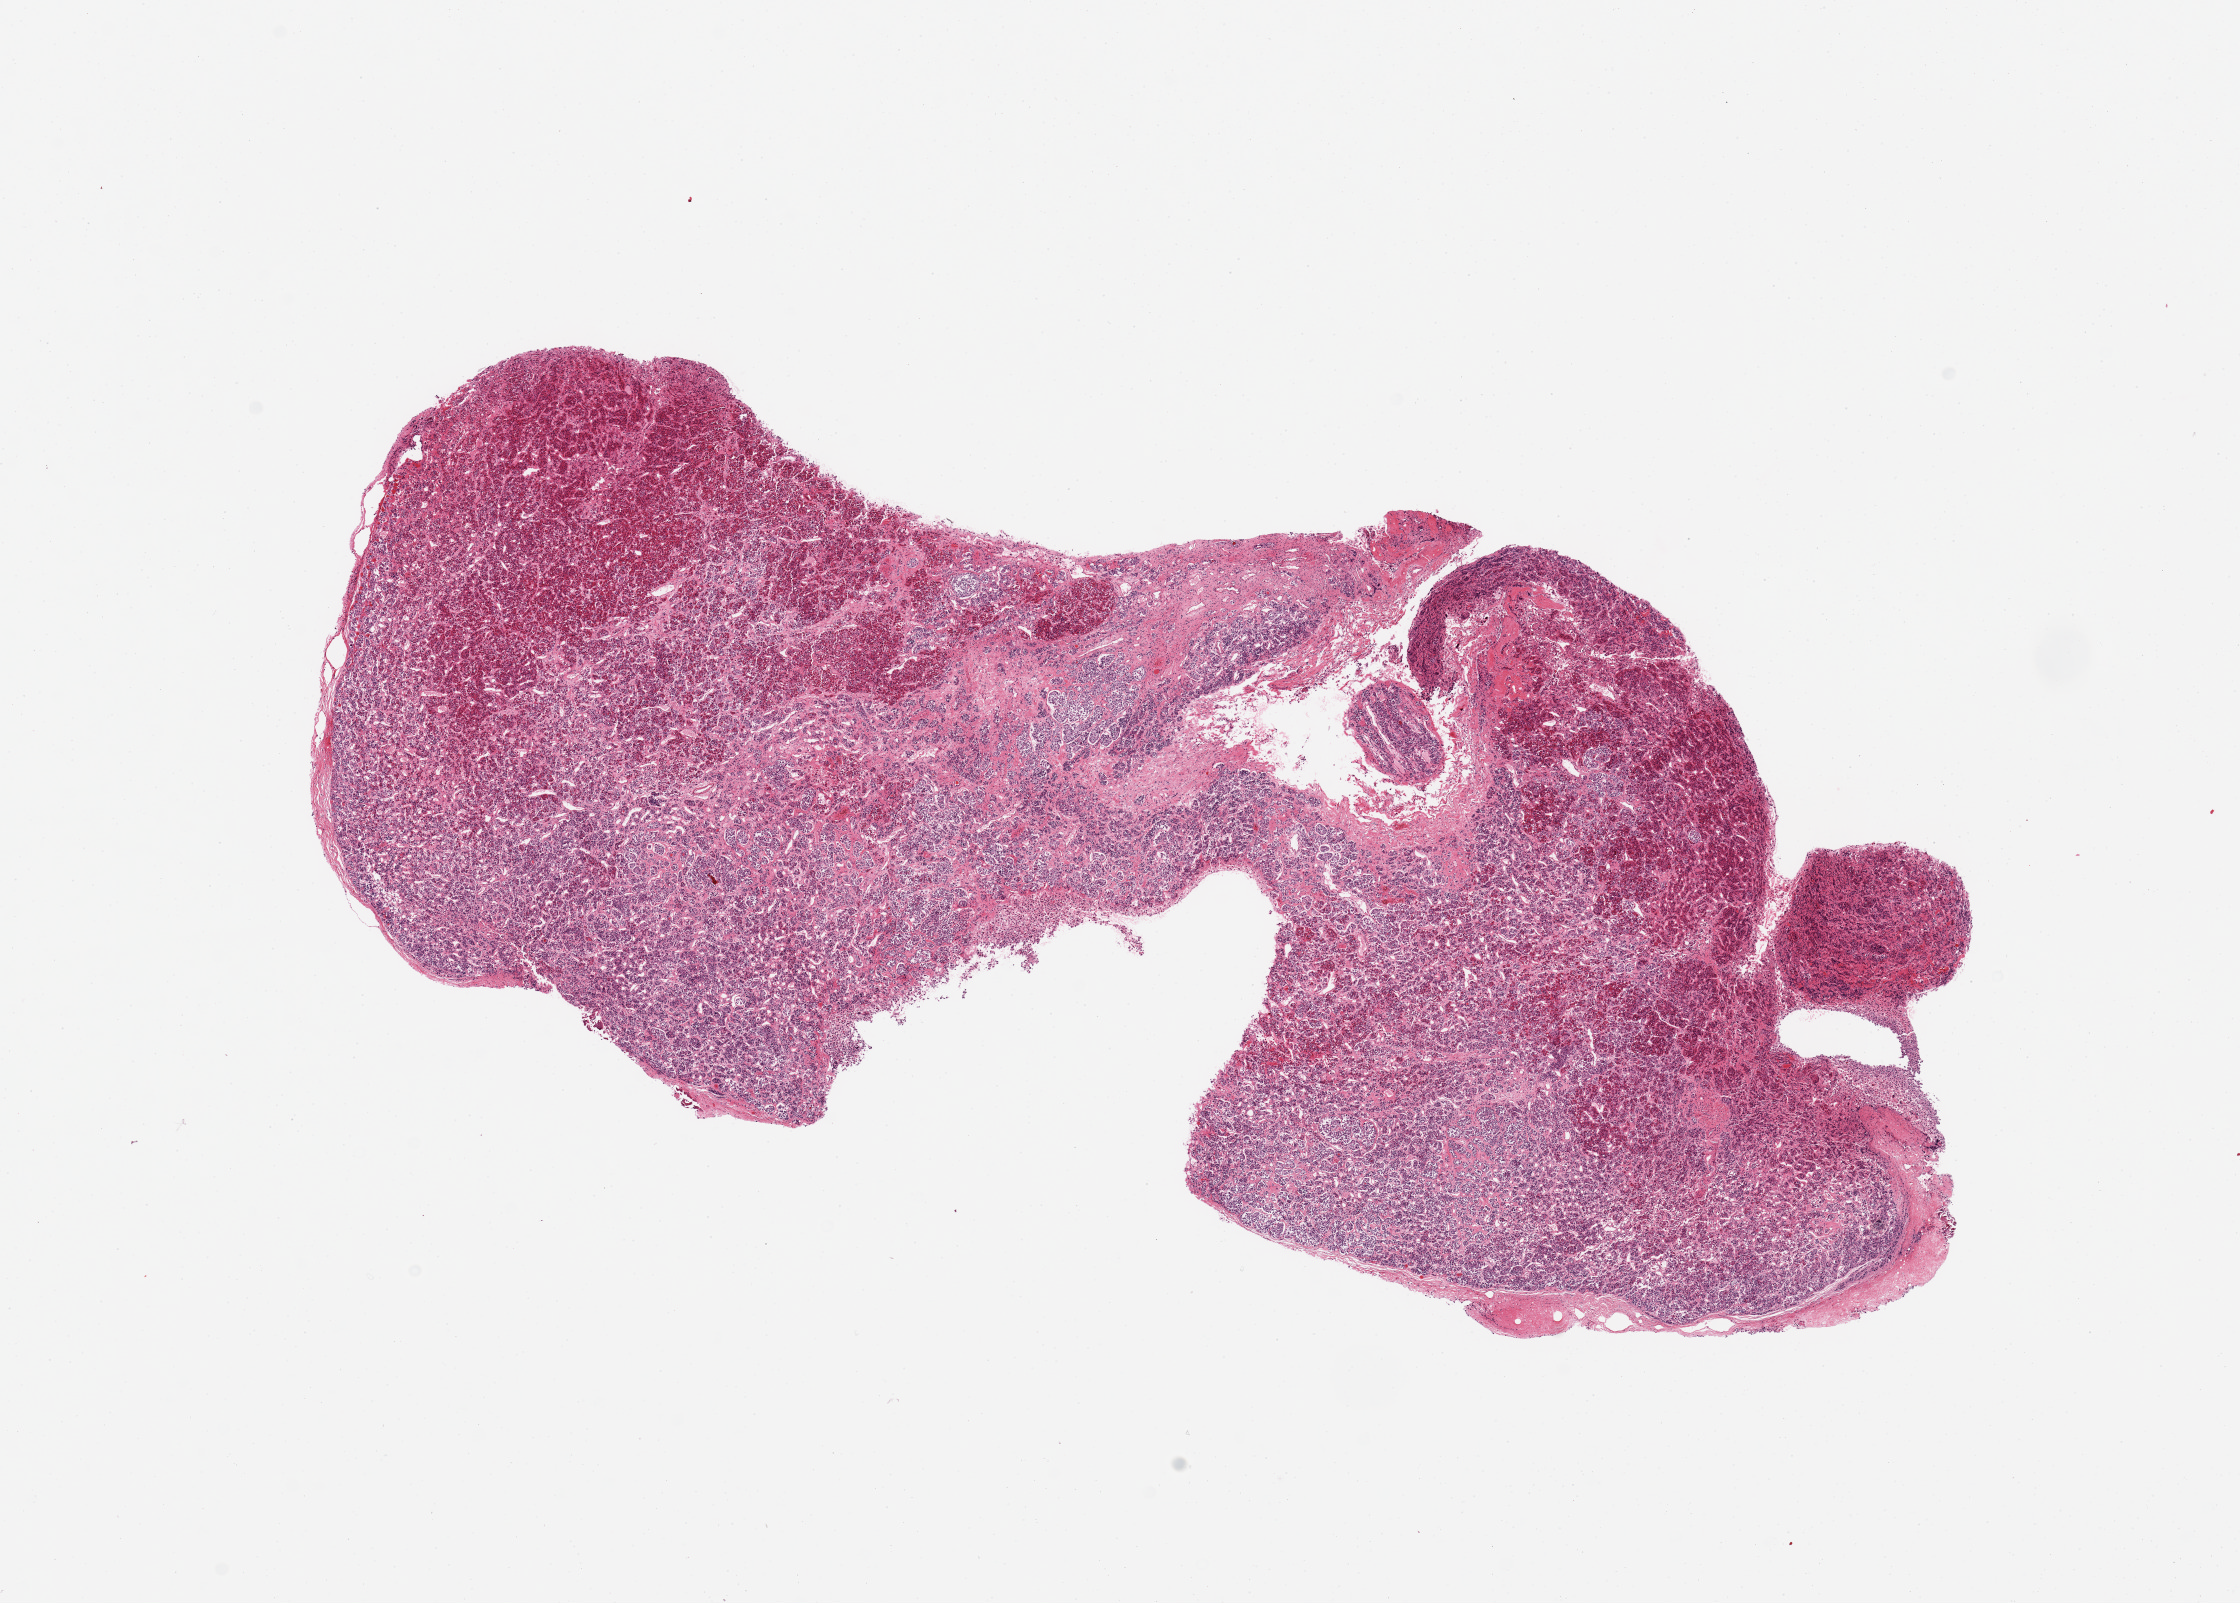
Digitized hematoxylin and eosin (H&E)-stained section, a low-resolution overview of the entire scanned area, about 17.7 x 12.7 mm. PAXgene-fixed, paraffin-embedded tissue. Target tissue: pituitary. Donor tissue sample. Donor: male.
* review note (as recorded): 1 piece, adenohypophysis